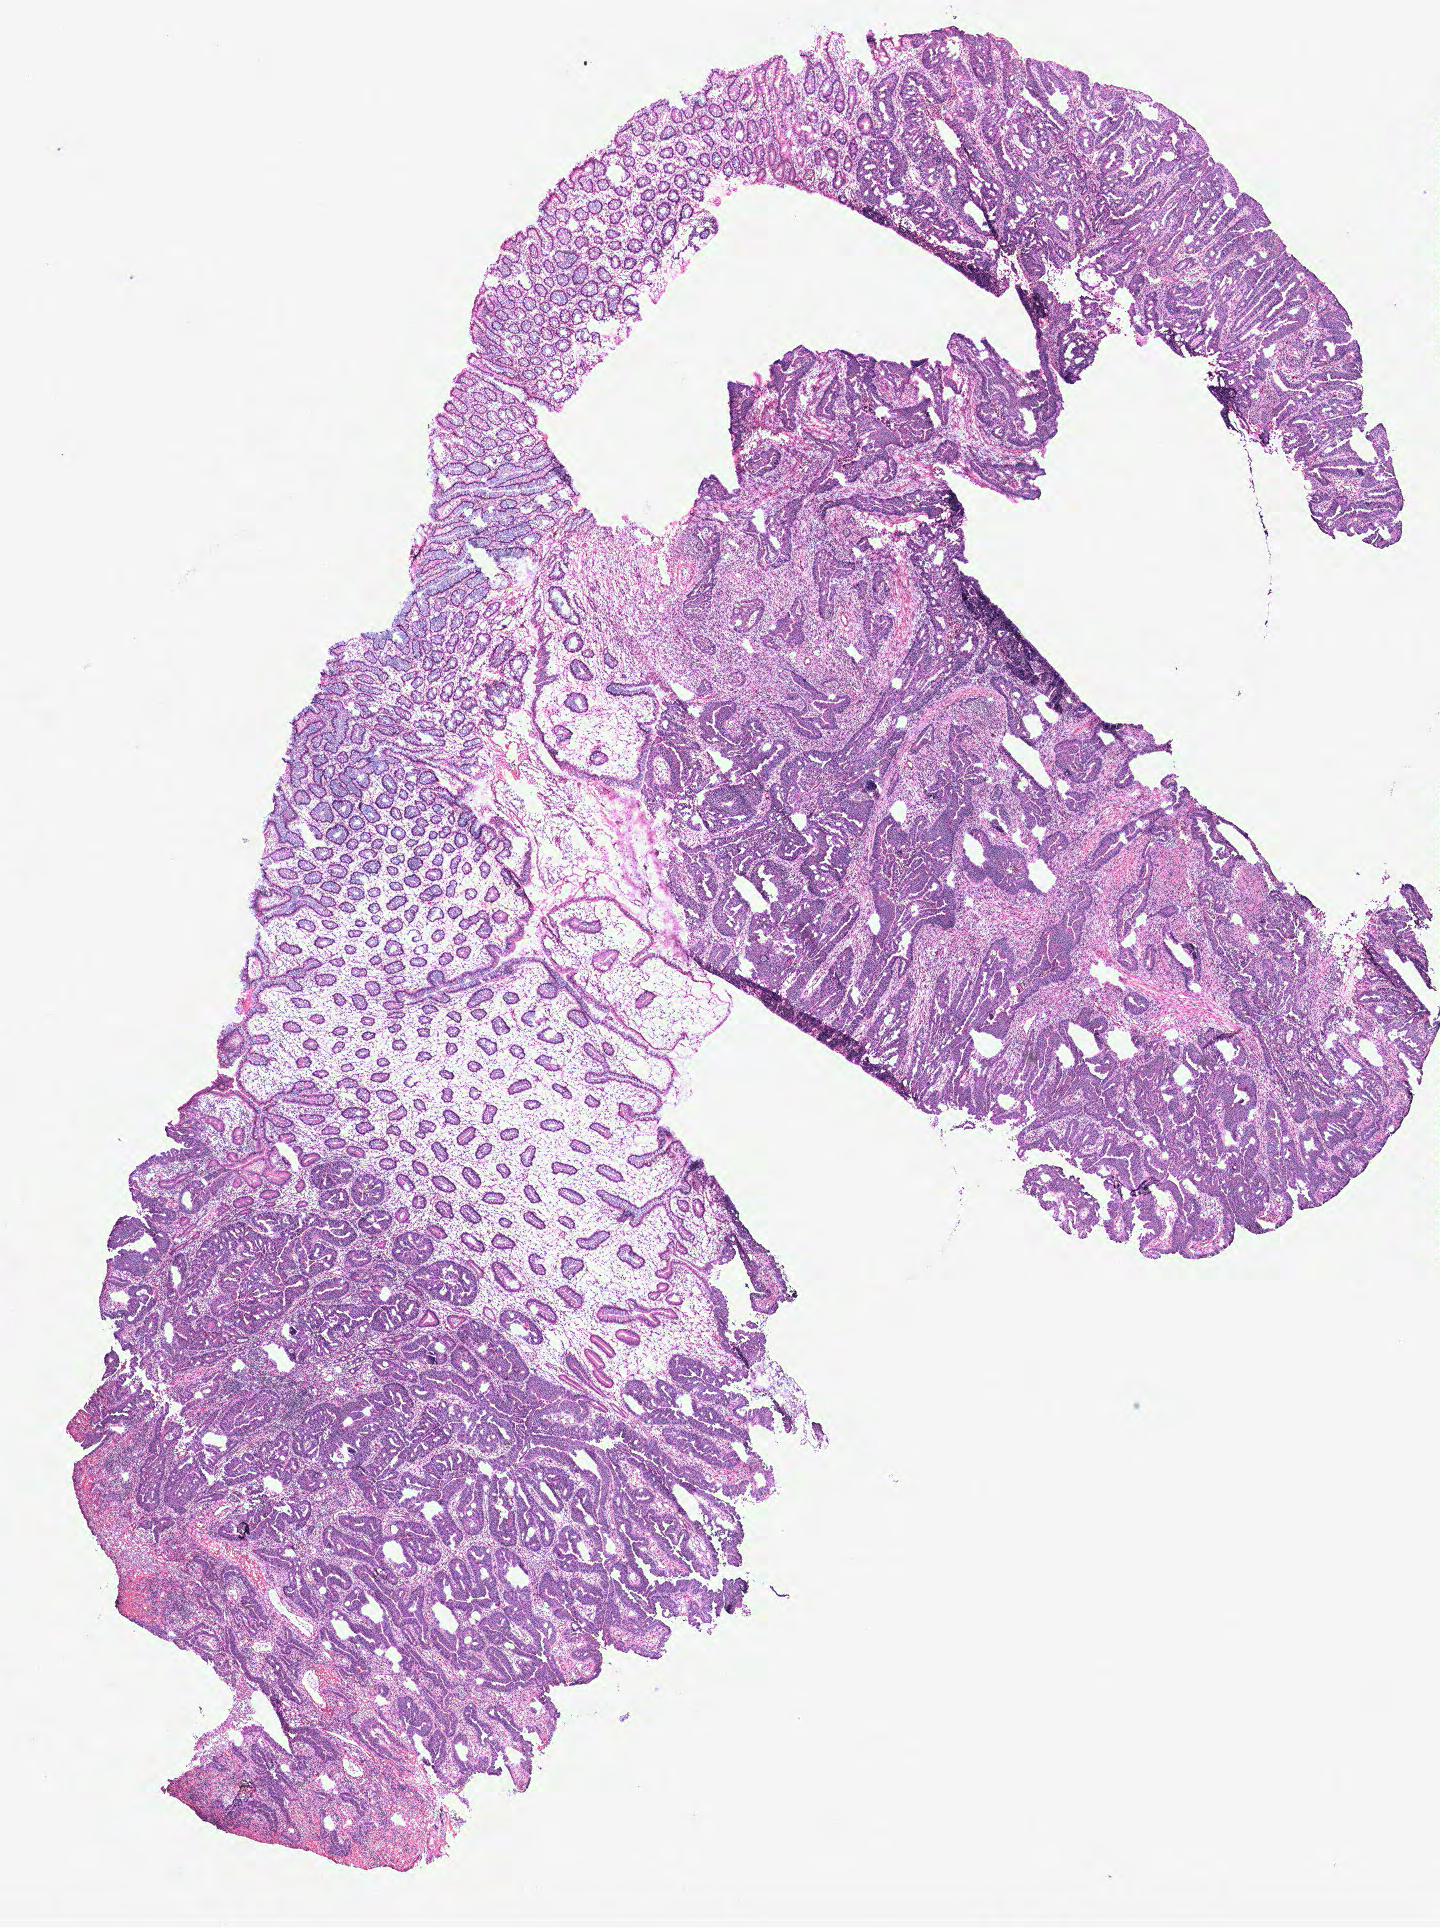
Whole-slide histology image, Hematoxylin and eosin (H&E) stained, a low-resolution overview of the entire scanned area, about 11.5 x 15.4 mm (from a 40x scan). Colon, tissue type not recorded.
Patient diagnosis (cohort enrolment): colon cancer (colon).